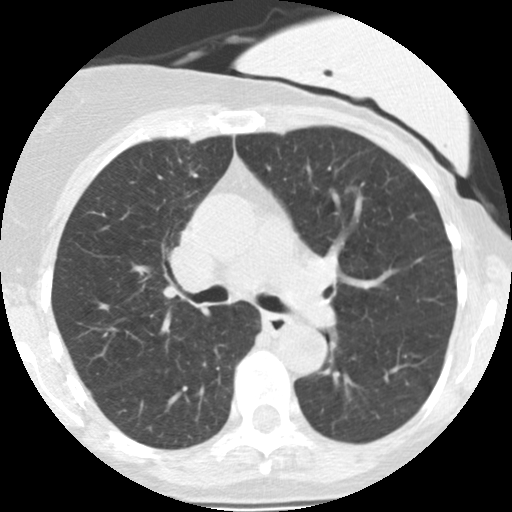
Axial slice from a low-dose chest CT screening exam; second annual screen; lung window (W 1500 / L -600 HU); 2.5 mm slice thickness; slice 96 of 251 in the series; 512 × 512 image matrix, field of view 280 × 280 mm. Female, age 66 years at enrolment. Former smoker at enrolment.
• Lesion marked by an expert reader, box from (x=342, y=181) to (x=361, y=203) px.
• Reader record for this screening exam (exam-level; its link to the box is not recorded): non-calcified nodule or mass ≥4 mm, left upper lobe, 7 × 5 mm, smooth margins, soft tissue attenuation, pre-existing on the prior screen: yes; interval growth: yes.
• Participant outcome: lung cancer diagnosed 218 days after this screen — adenocarcinoma, NOS, left lower lobe, poorly differentiated (G3), stage IA (AJCC 6th edition), 8 mm at pathology.